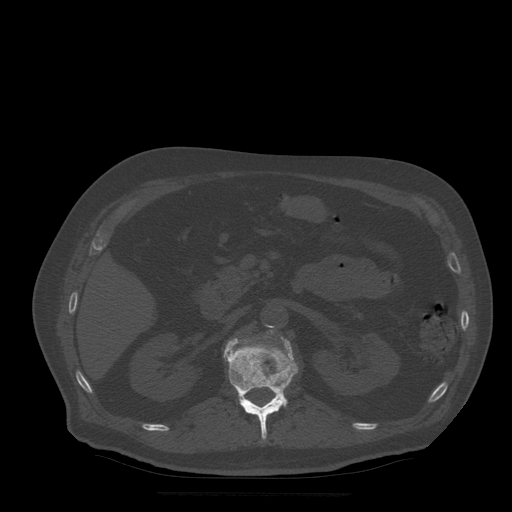
CT including the spine, one axial slice. Slice 192 of 522 in the series (ordered by position). Bone window (W 1800 / L 400 HU). 1.25 mm slice thickness. 512 × 512 image matrix, field of view 420 × 420 mm. Patient age 72 years. From the clinical record (not read from this slice): primary cancer: prostate.
Outlined on this slice (semi-automatically segmented with operator editing):
- L1 vertebra: bounding box (x1, y1, x2, y2) in pixels: (224, 337, 299, 440)
- L2 vertebra: (269, 330, 273, 333)